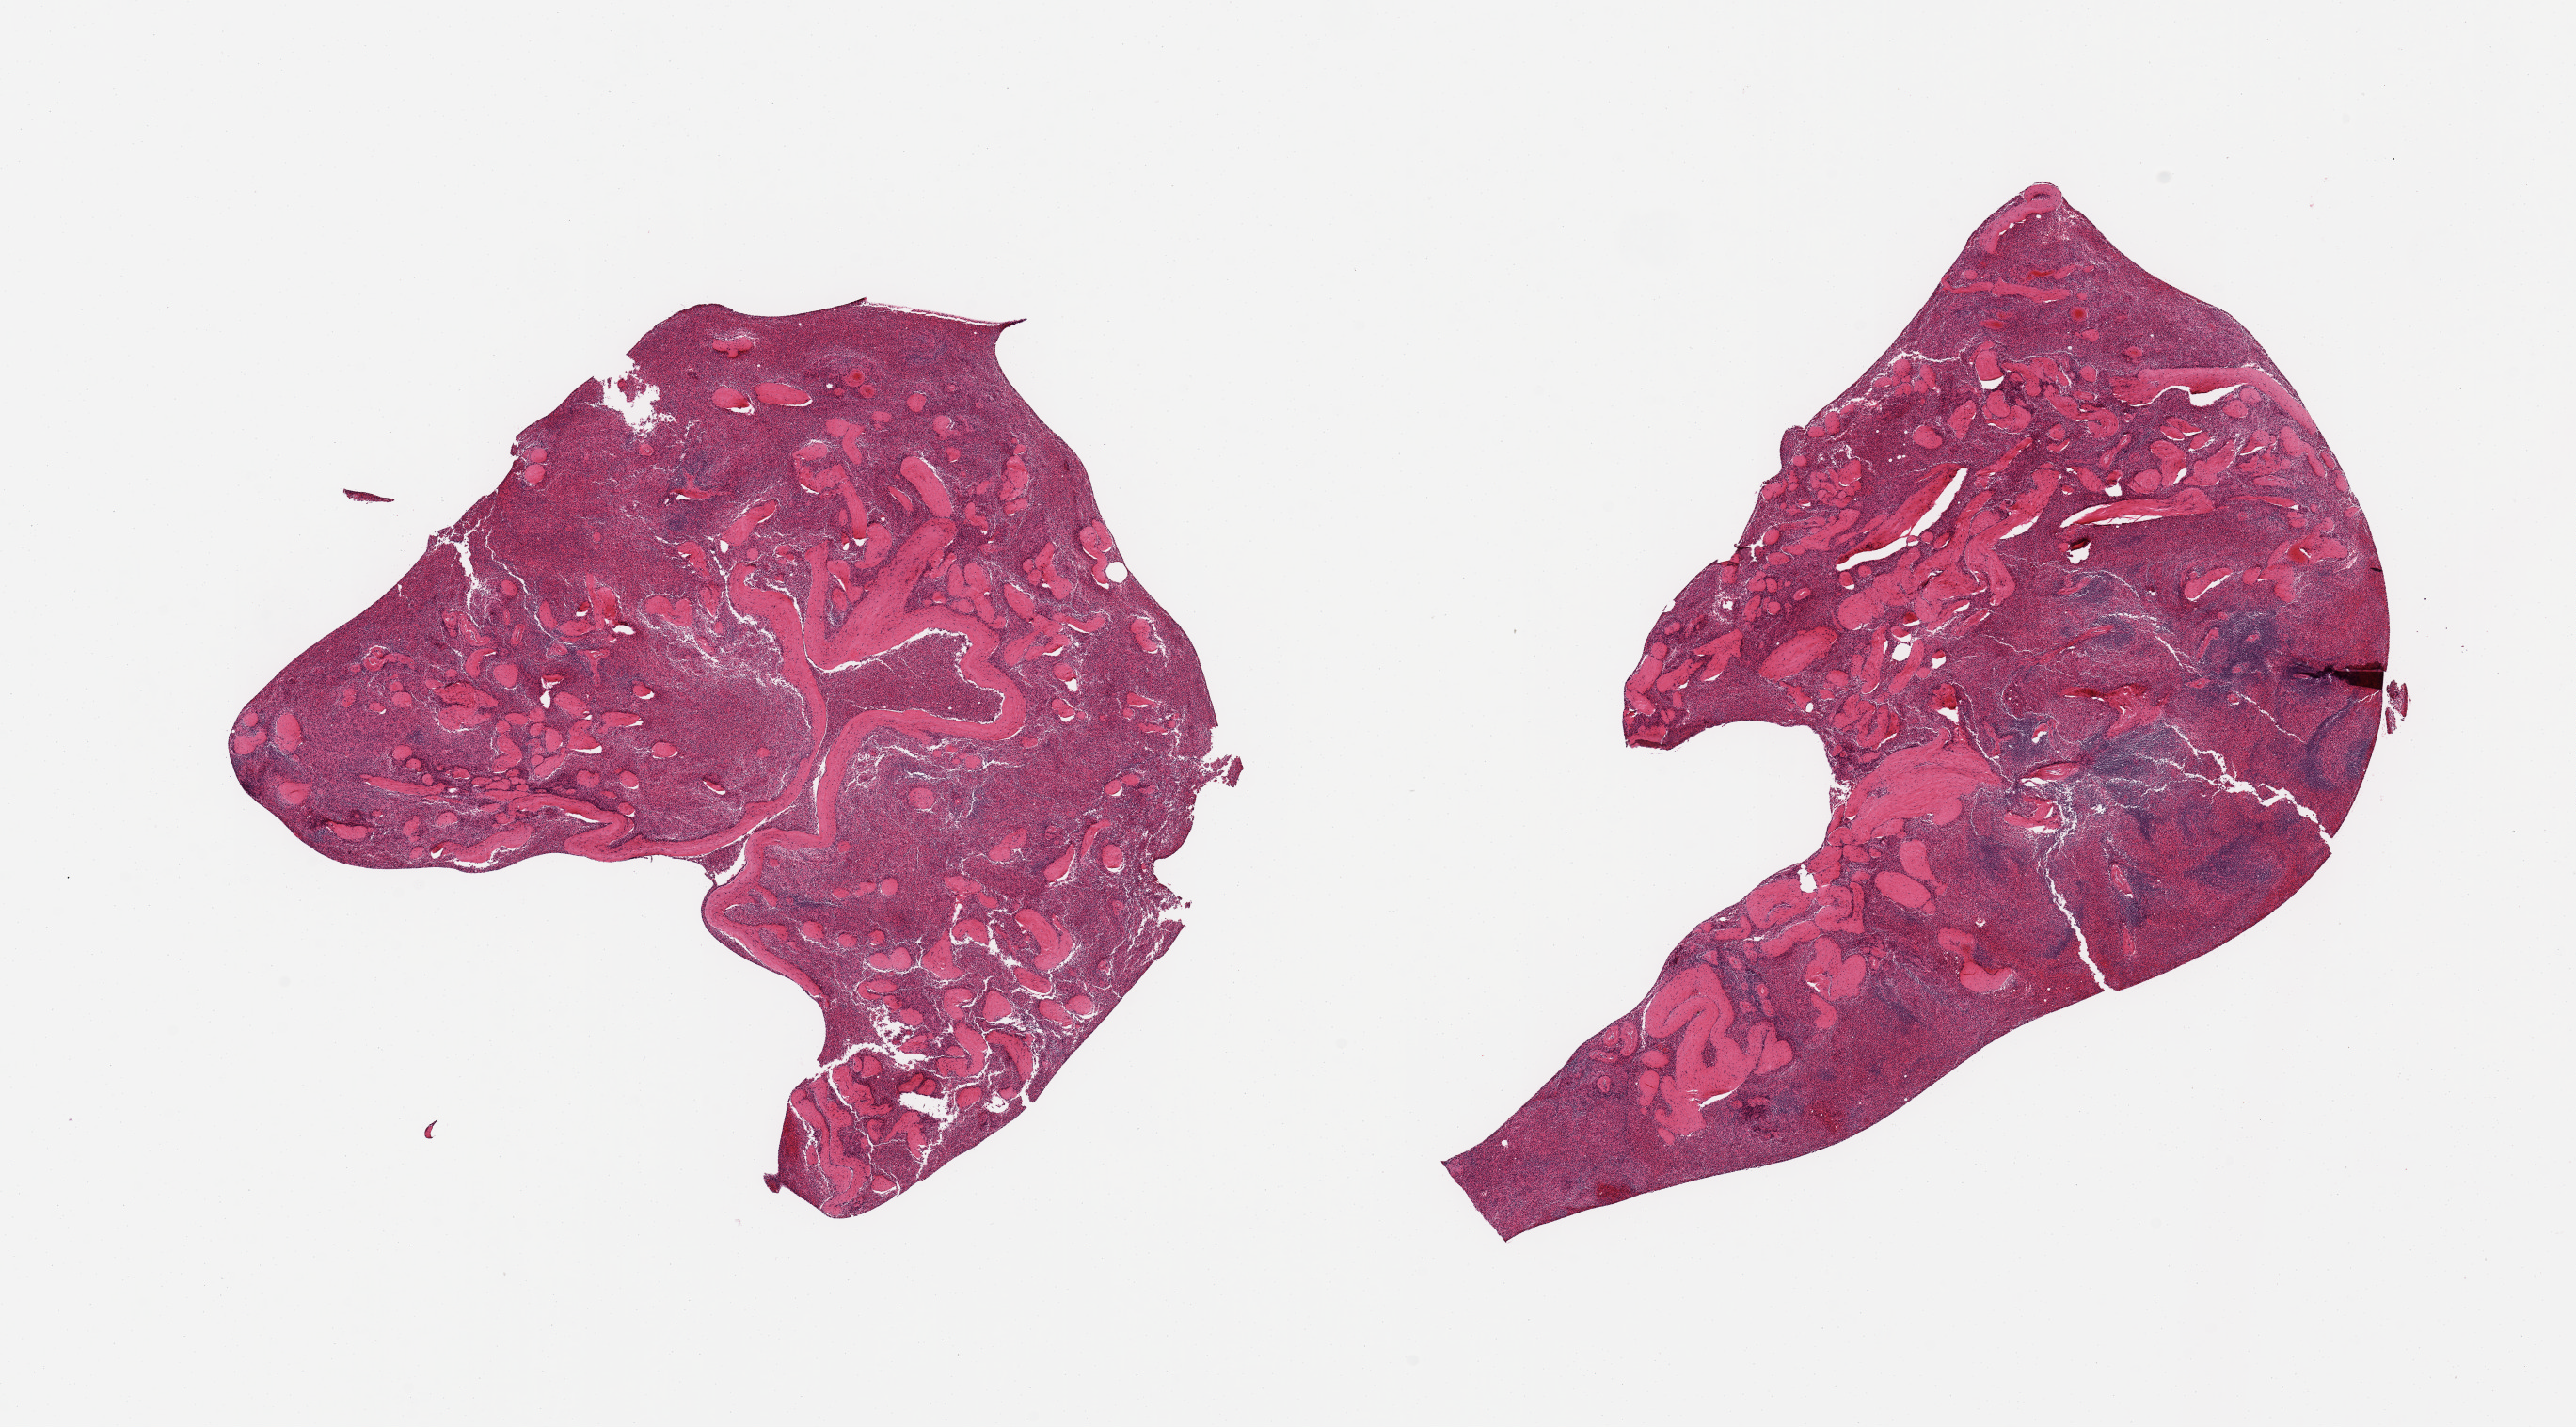
Whole-slide image, hematoxylin and eosin (H&E) stain, brightfield, low-resolution overview of the scanned area, about 21.7 x 12.0 mm, PAXgene-fixed, paraffin-embedded tissue, section of spleen (target tissue), donor tissue sample. Donor sex: male.
- pathologist's review note for this sample: 2 pieces; congested white and red pulp with prominent fibrous trabeculae